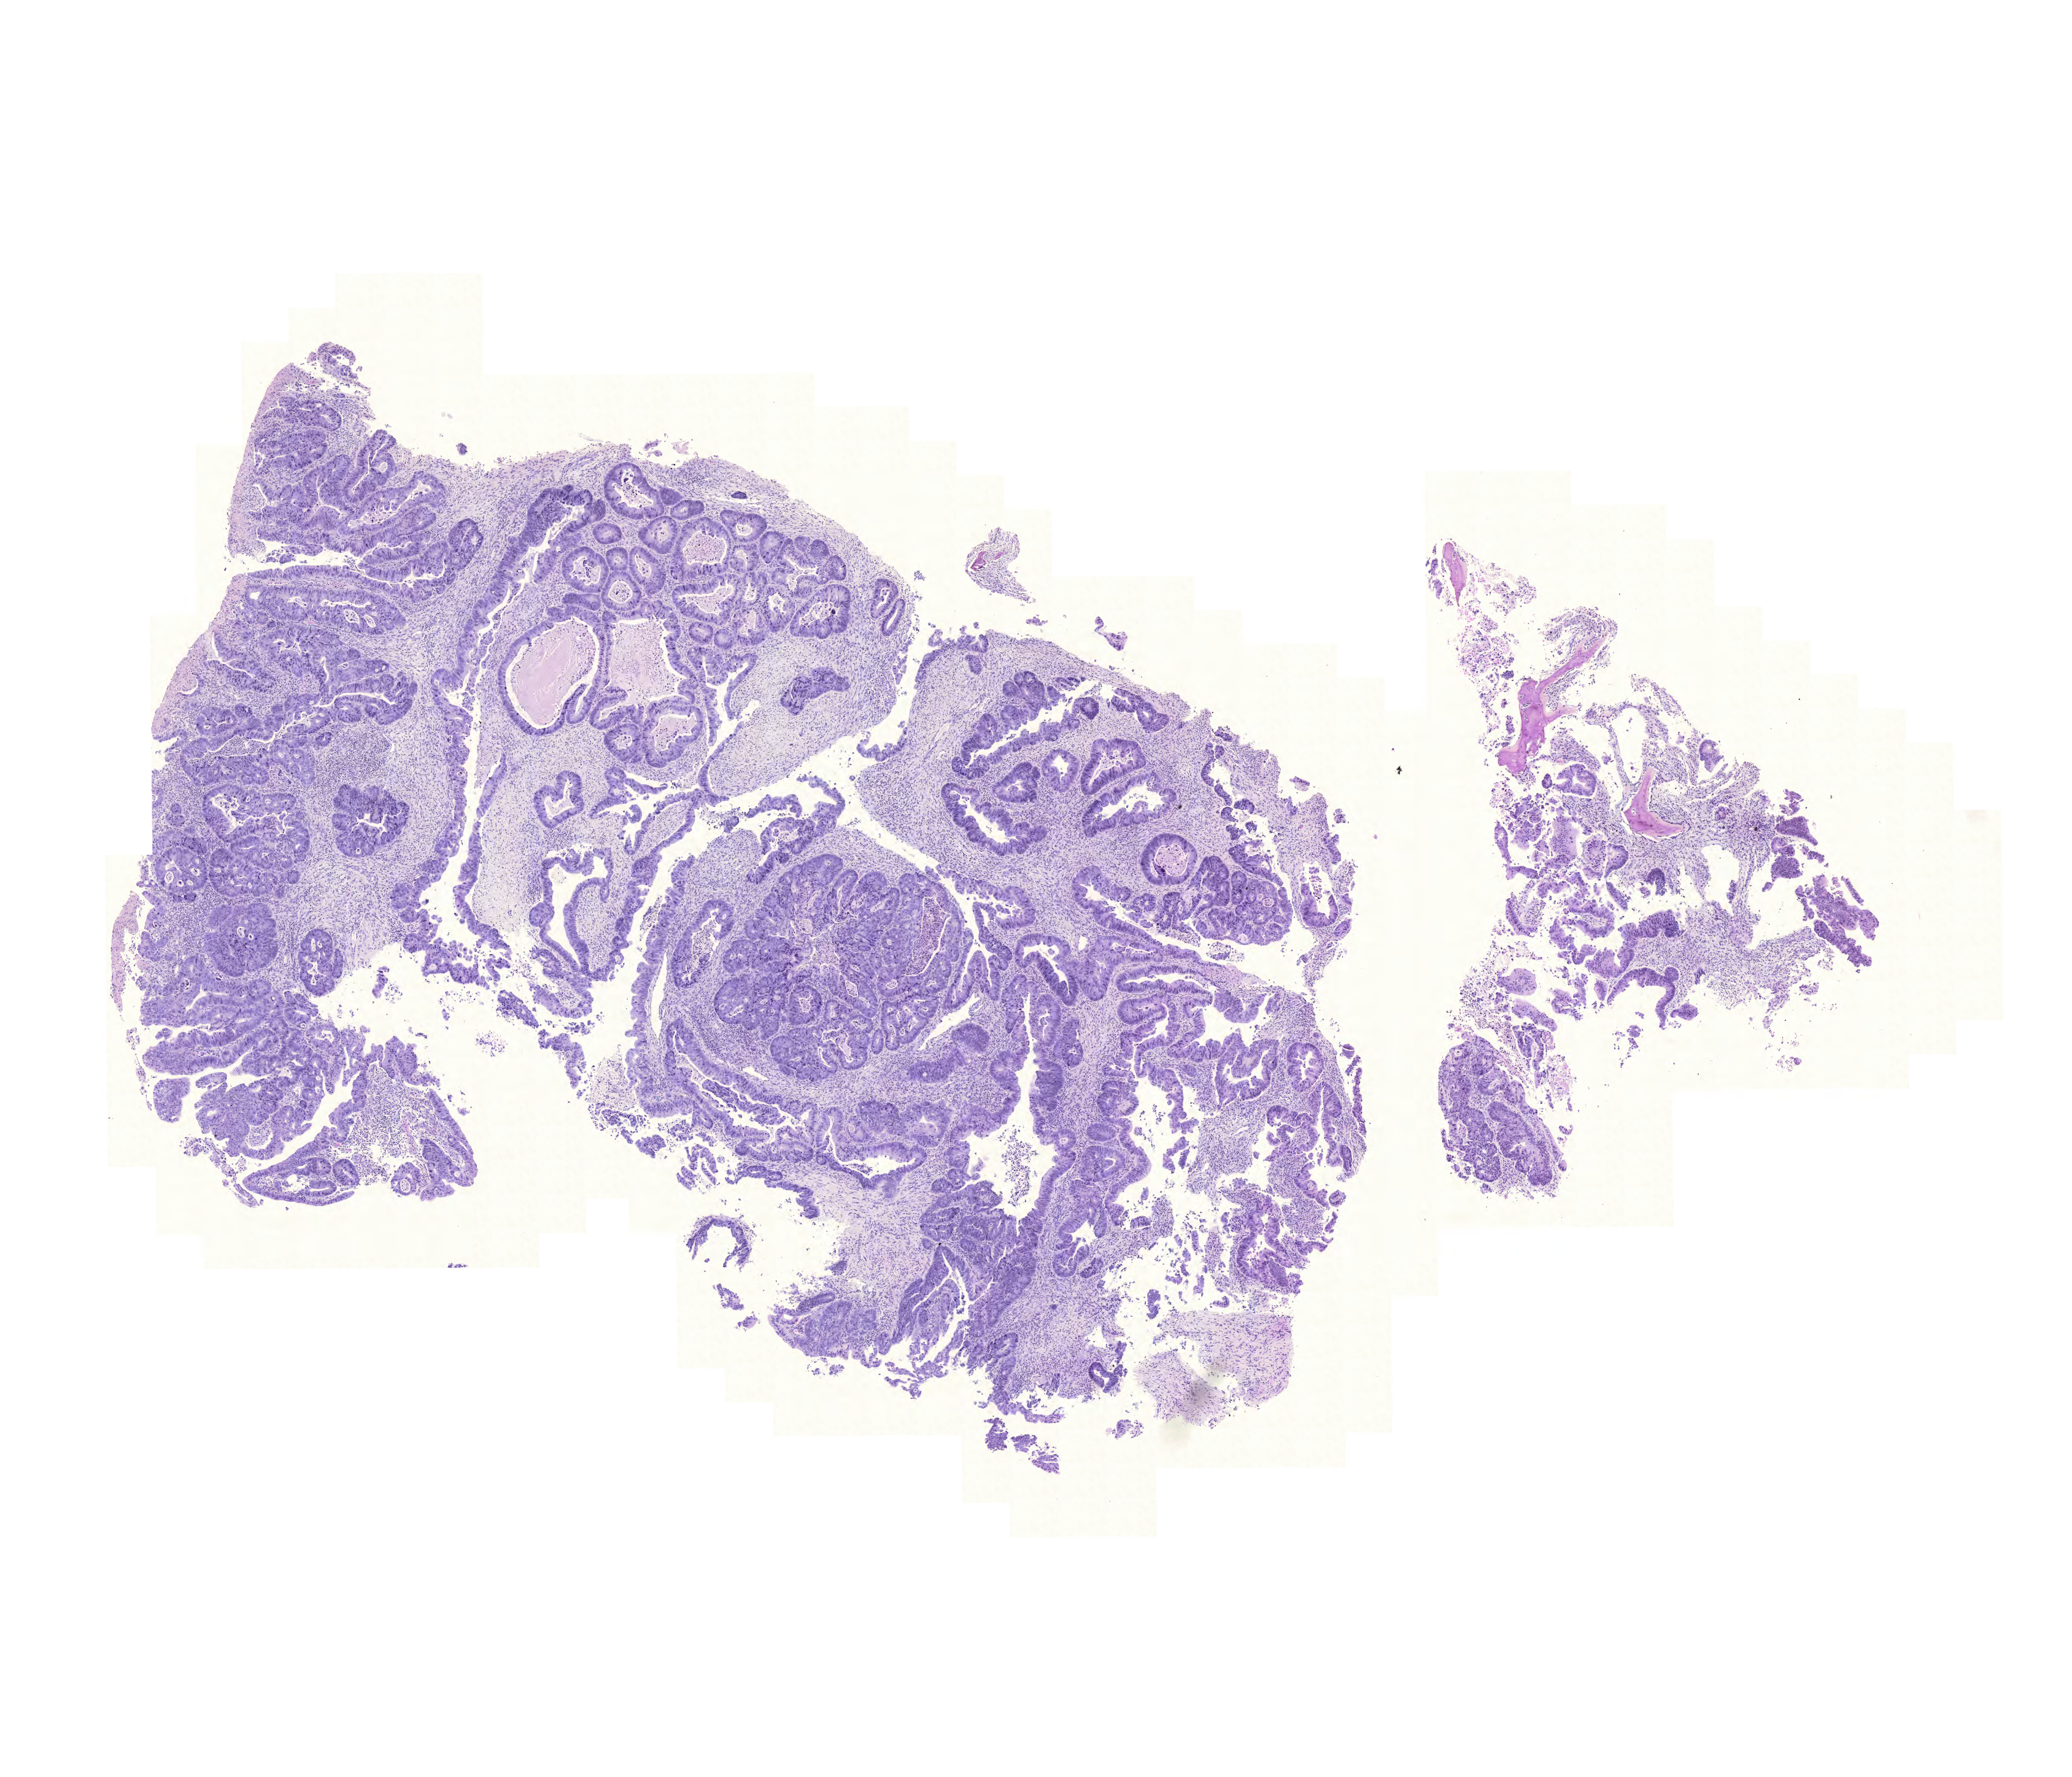
Whole-slide histology image, Hematoxylin and eosin (H&E) stained, a low-resolution overview of the entire scanned area, about 12.6 x 10.8 mm (from a 20x scan). Formalin-fixed paraffin-embedded (FFPE) diagnostic section. Sample: primary tumour, colon. Male patient; age at initial diagnosis 76 years.
AJCC pathologic stage: IV. Lymph nodes positive (case pathology): 14 of 28 examined. Histologic diagnosis: Adenocarcinoma, NOS.